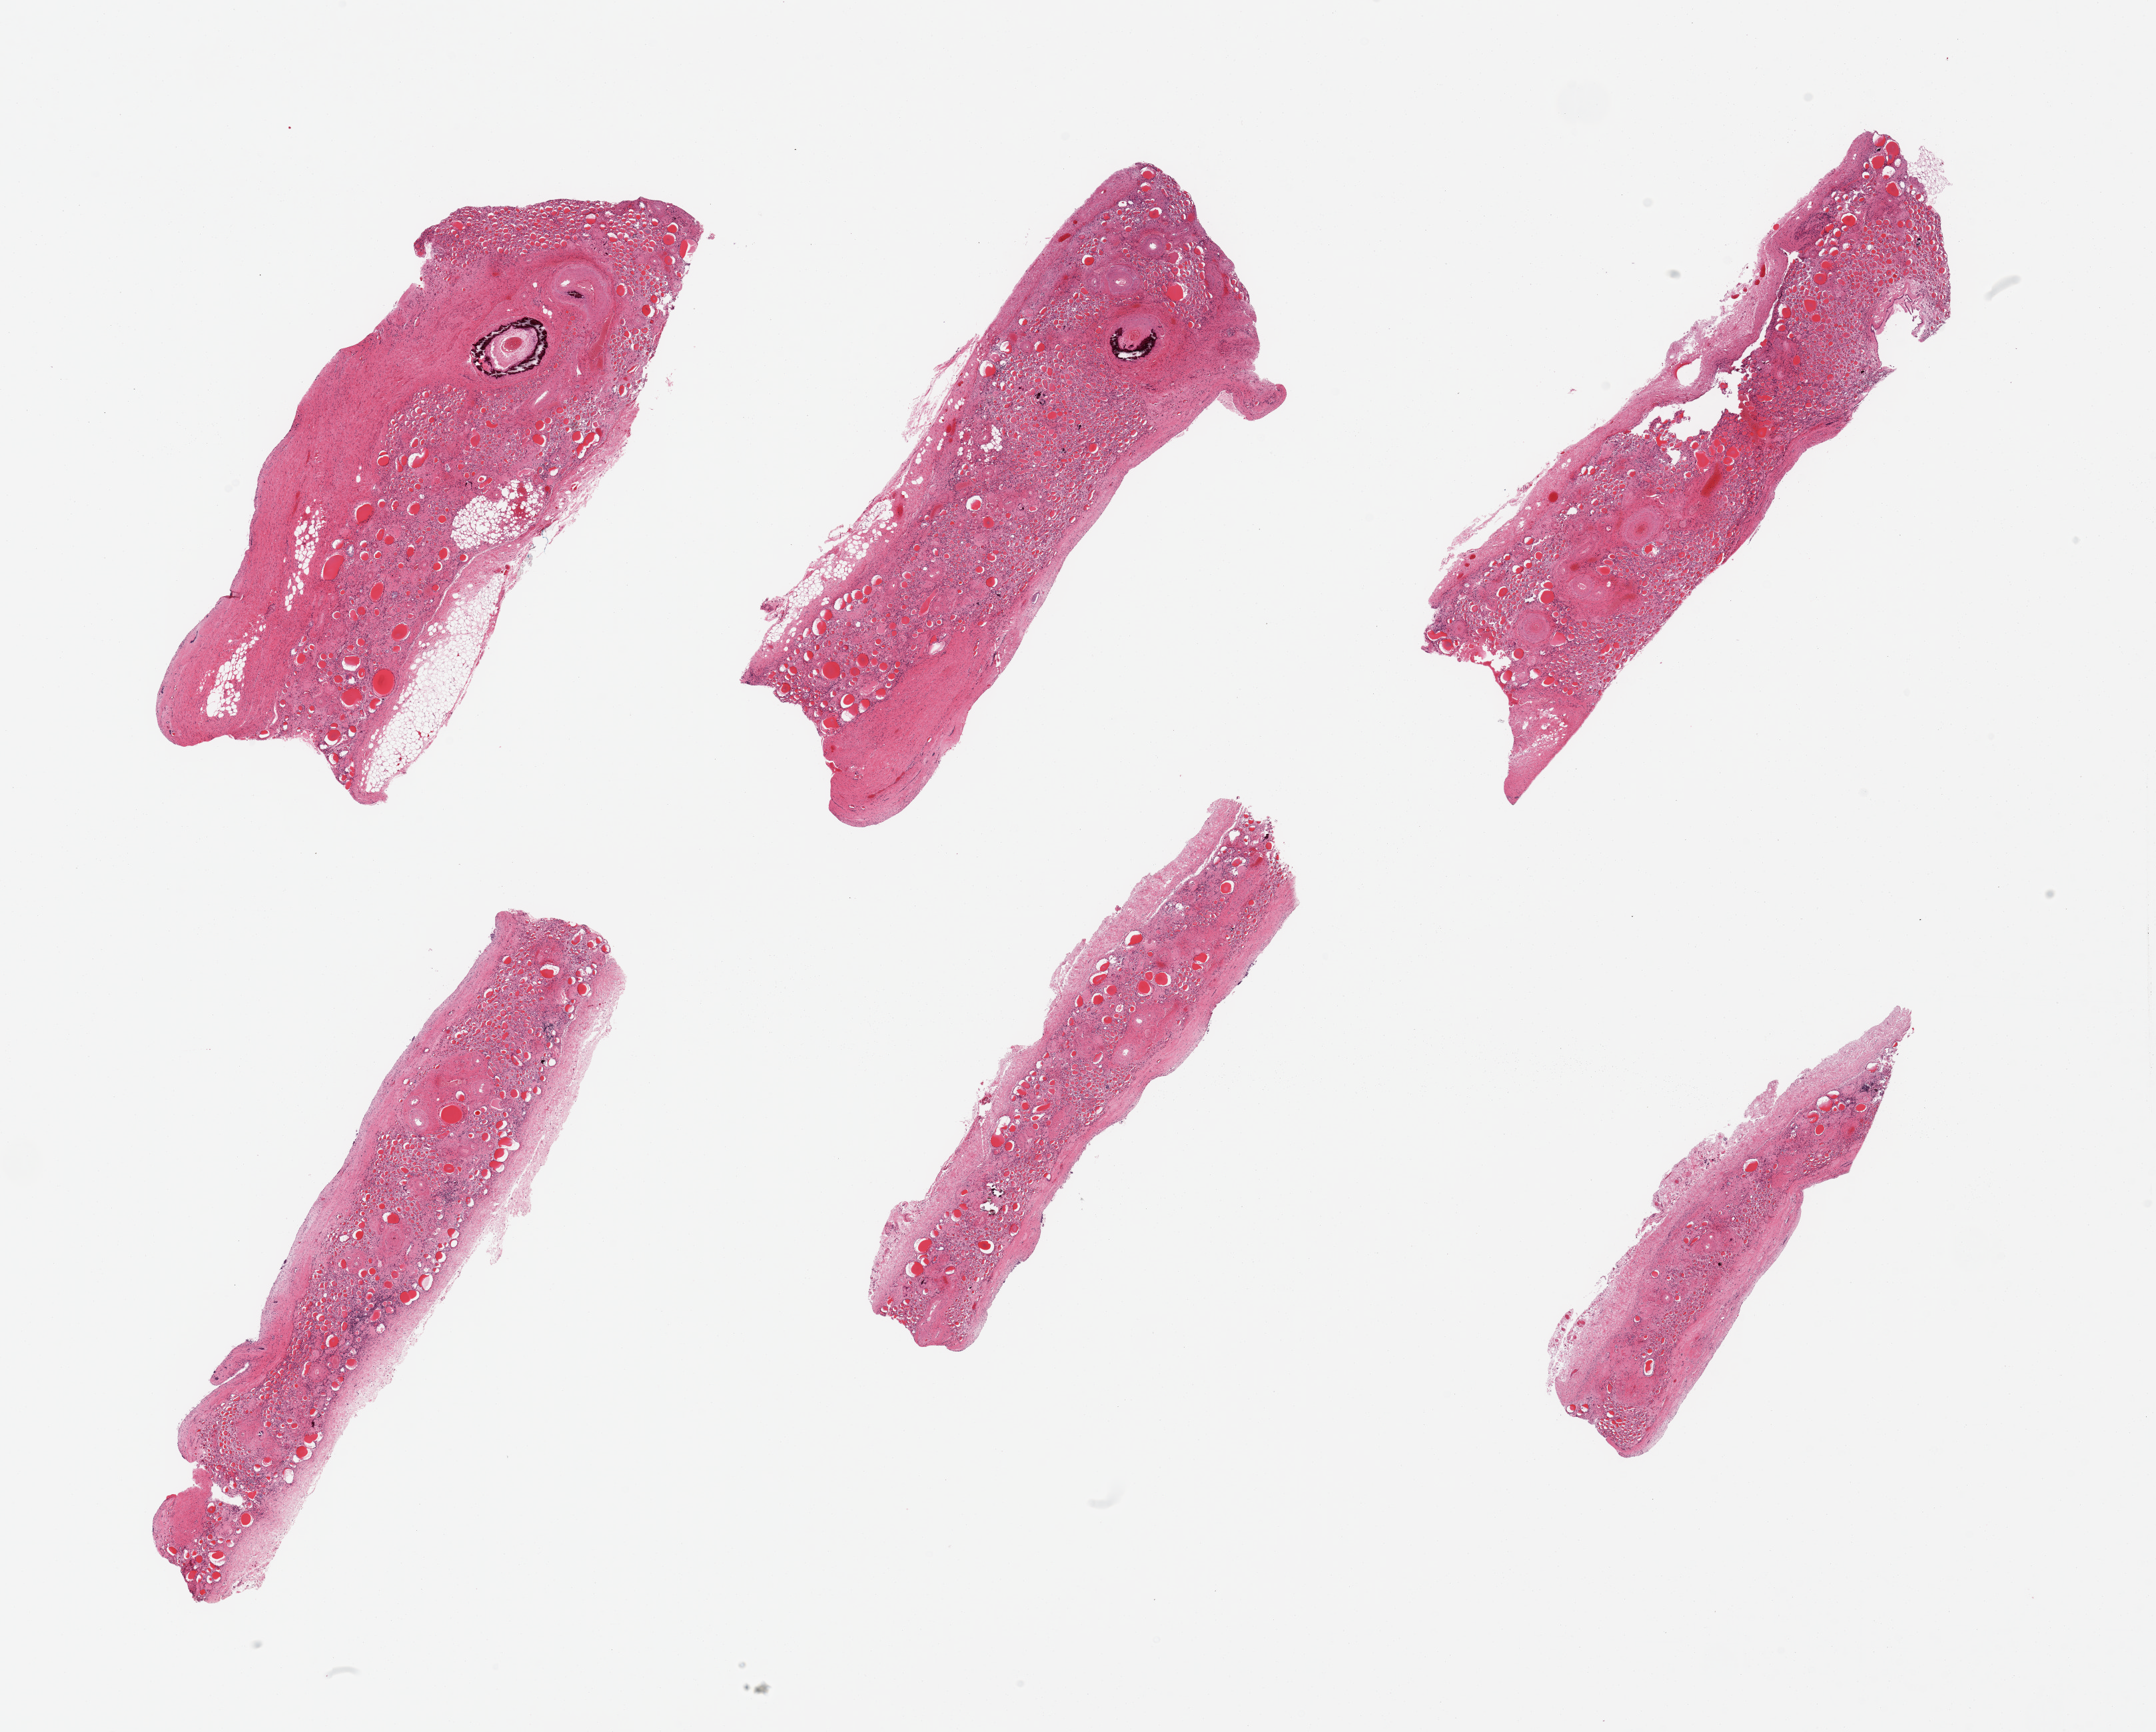
Whole-slide image, haematoxylin and eosin stain — low-resolution overview of the scanned area, about 25.6 x 20.6 mm (from a 20x scan); PAXgene-fixed, paraffin-embedded tissue; sampled site (target tissue): renal cortex; donor tissue sample. Female donor.
• review note (as recorded): 6 pieces, advanced chroinic neprhritis, probably vasculopathic, with thyroidization and severe hyalinizing glomerulosclerosis